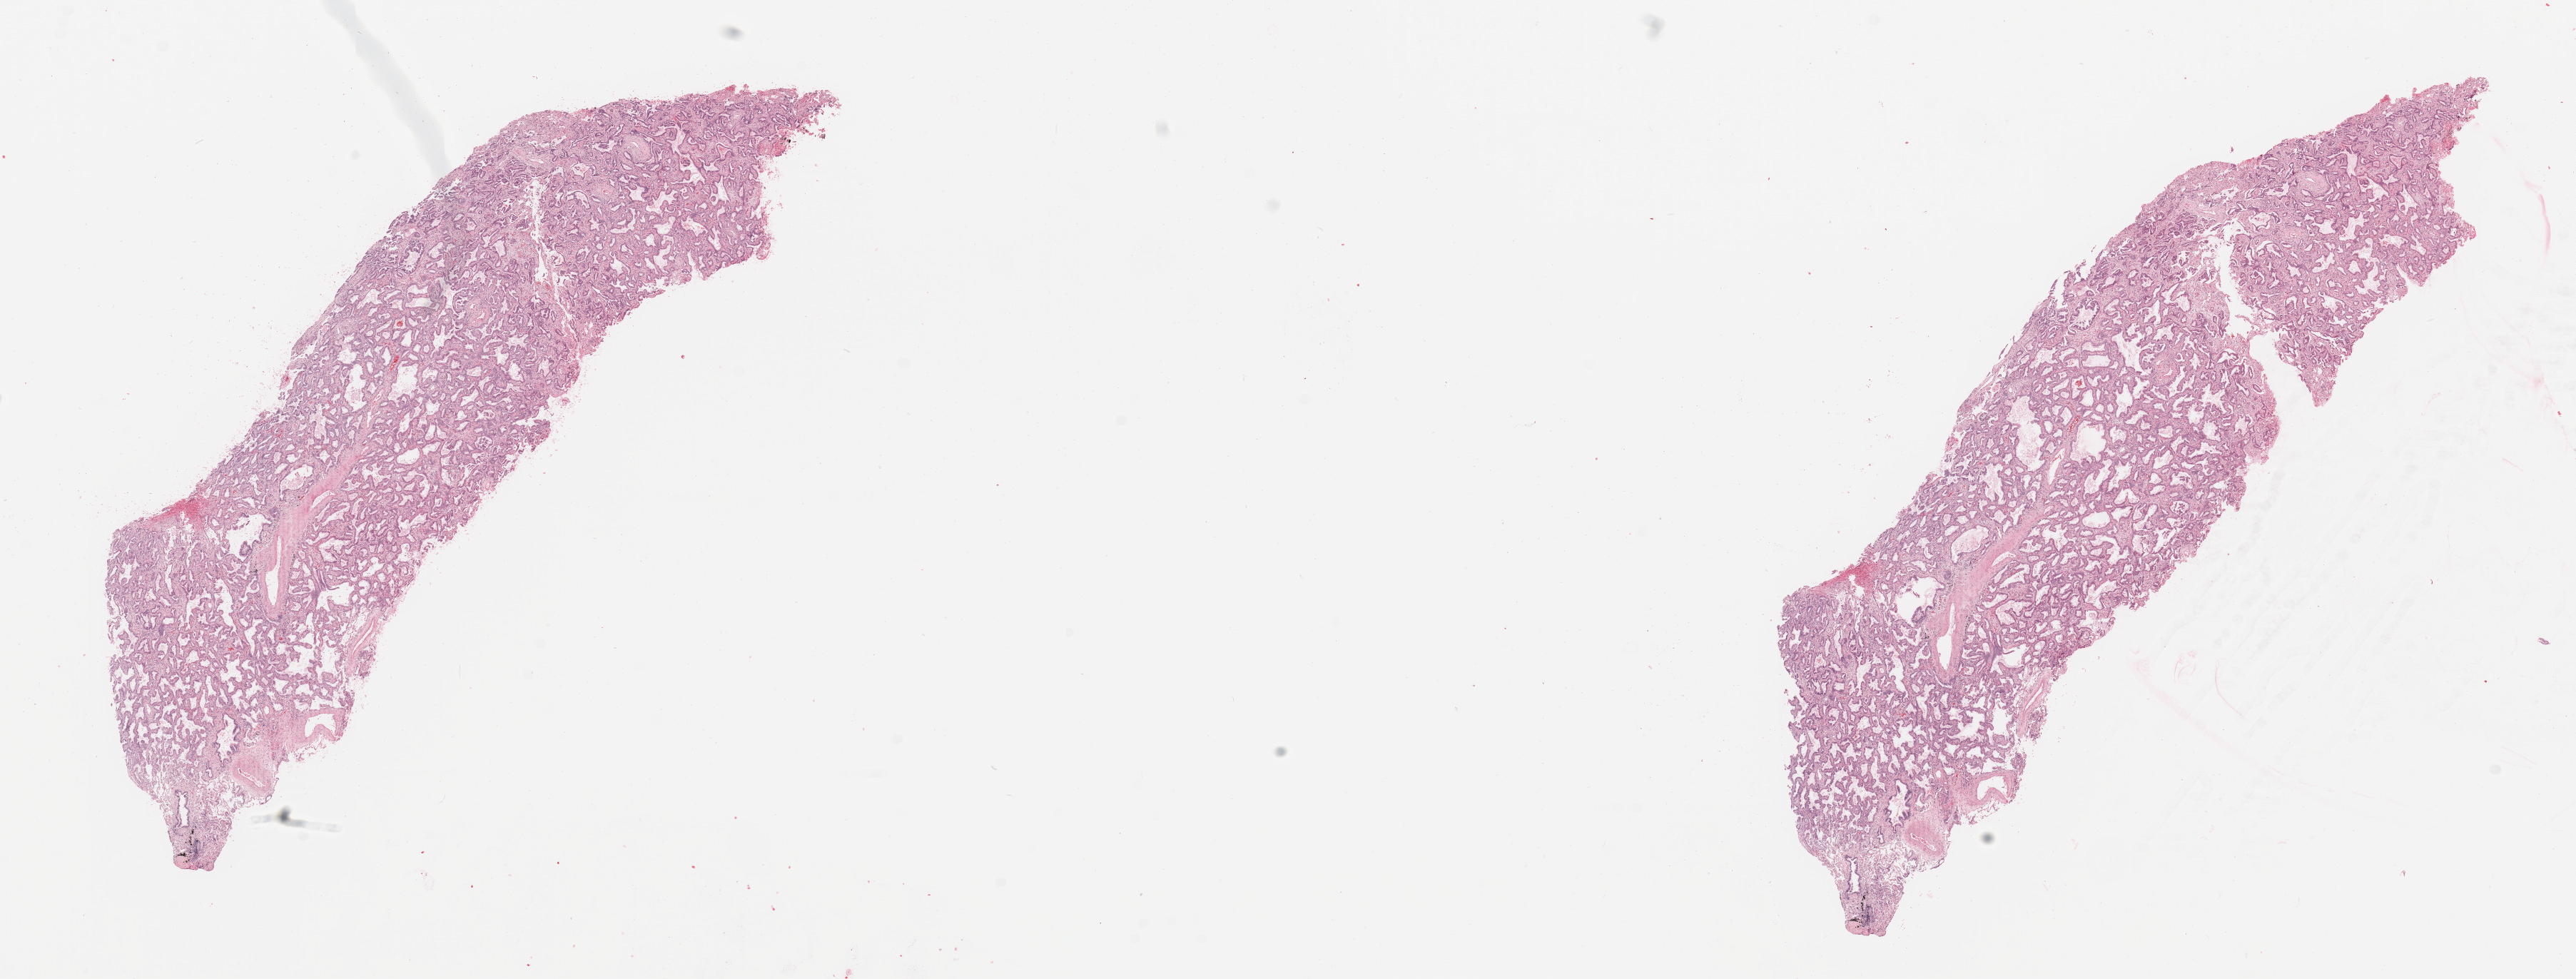
Hematoxylin and eosin (H&E) stained whole-slide image, a low-resolution overview of the entire scanned area, about 28.5 x 10.8 mm (acquisition: 20x scan), lung, tumour tissue. 78-year-old male patient. Histologic grade: G1 (well differentiated).
Diagnosis: Adenocarcinoma, NOS. Primary tumour site (as recorded): right lower lobe. AJCC pathologic stage: IA.